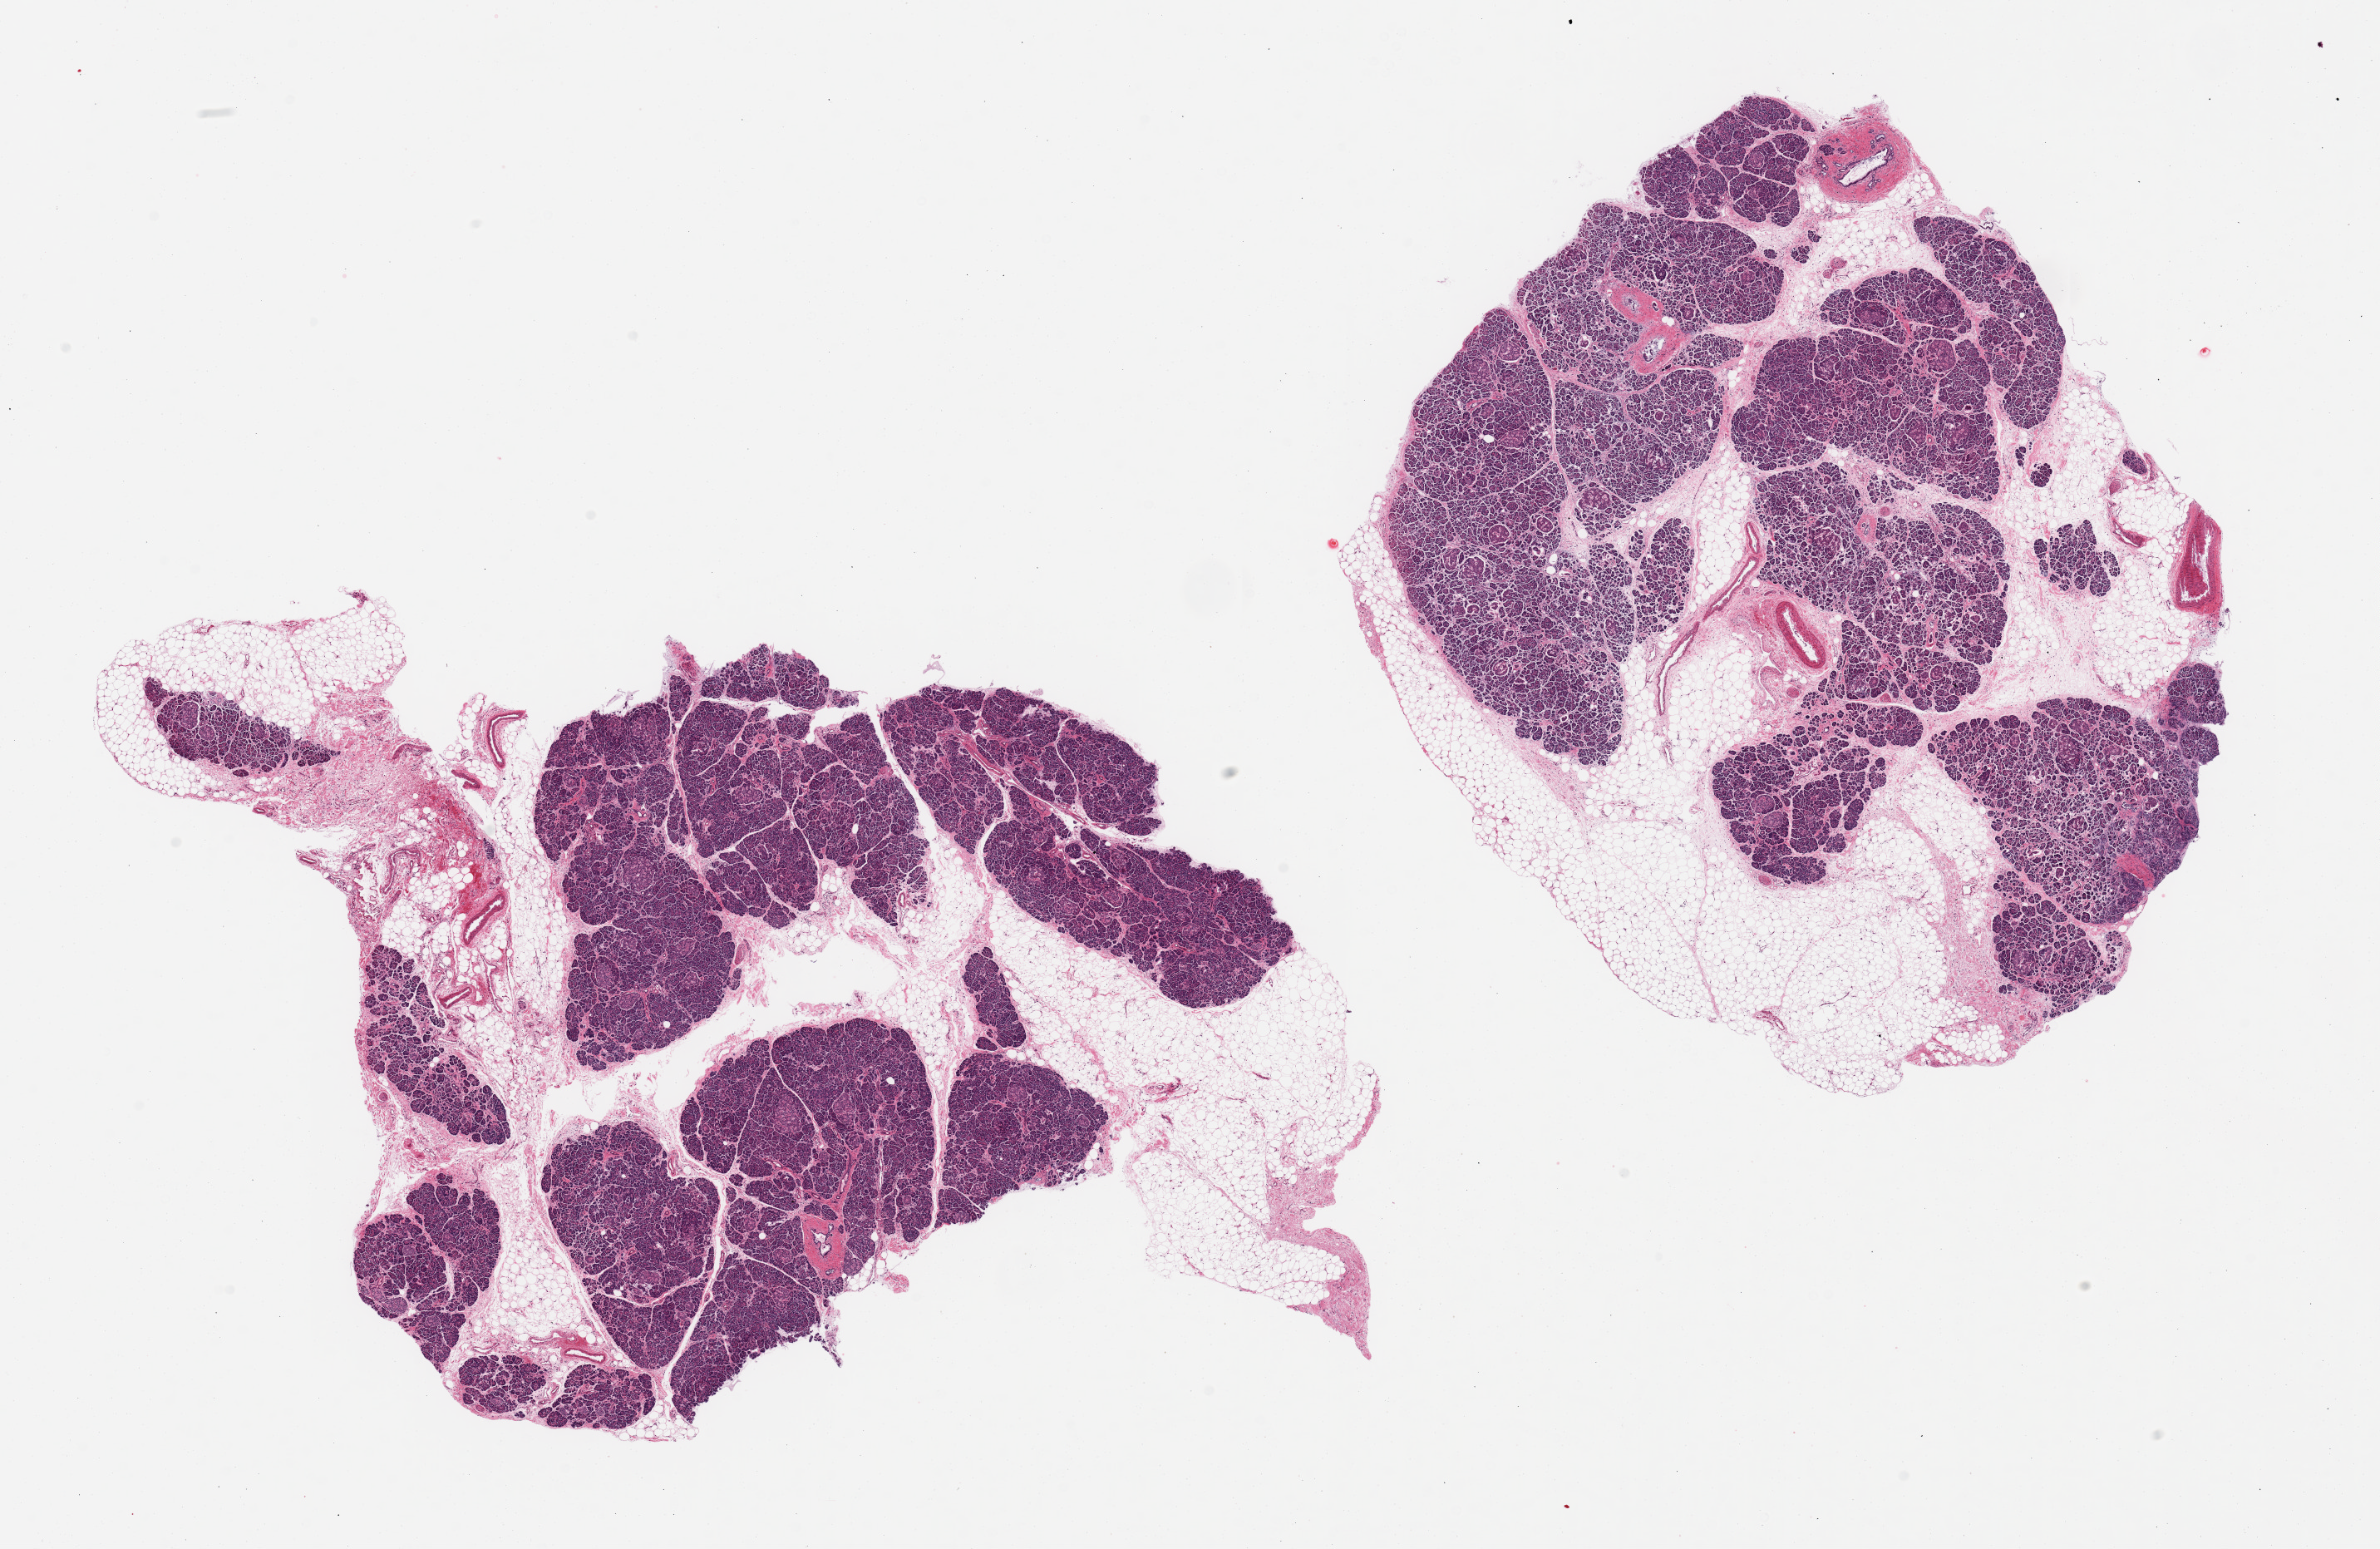
Hematoxylin and eosin (H&E) whole-slide image, shown as a low-resolution overview of the whole scanned area (about 22.6 x 14.7 mm, from a 20x scan). PAXgene-fixed, paraffin-embedded tissue. Sampled site (target tissue): pancreas. Donor tissue sample.
Pathologist's review note for this sample: 2 pieces; islets are only slightly autolyzed; 40% fat content.